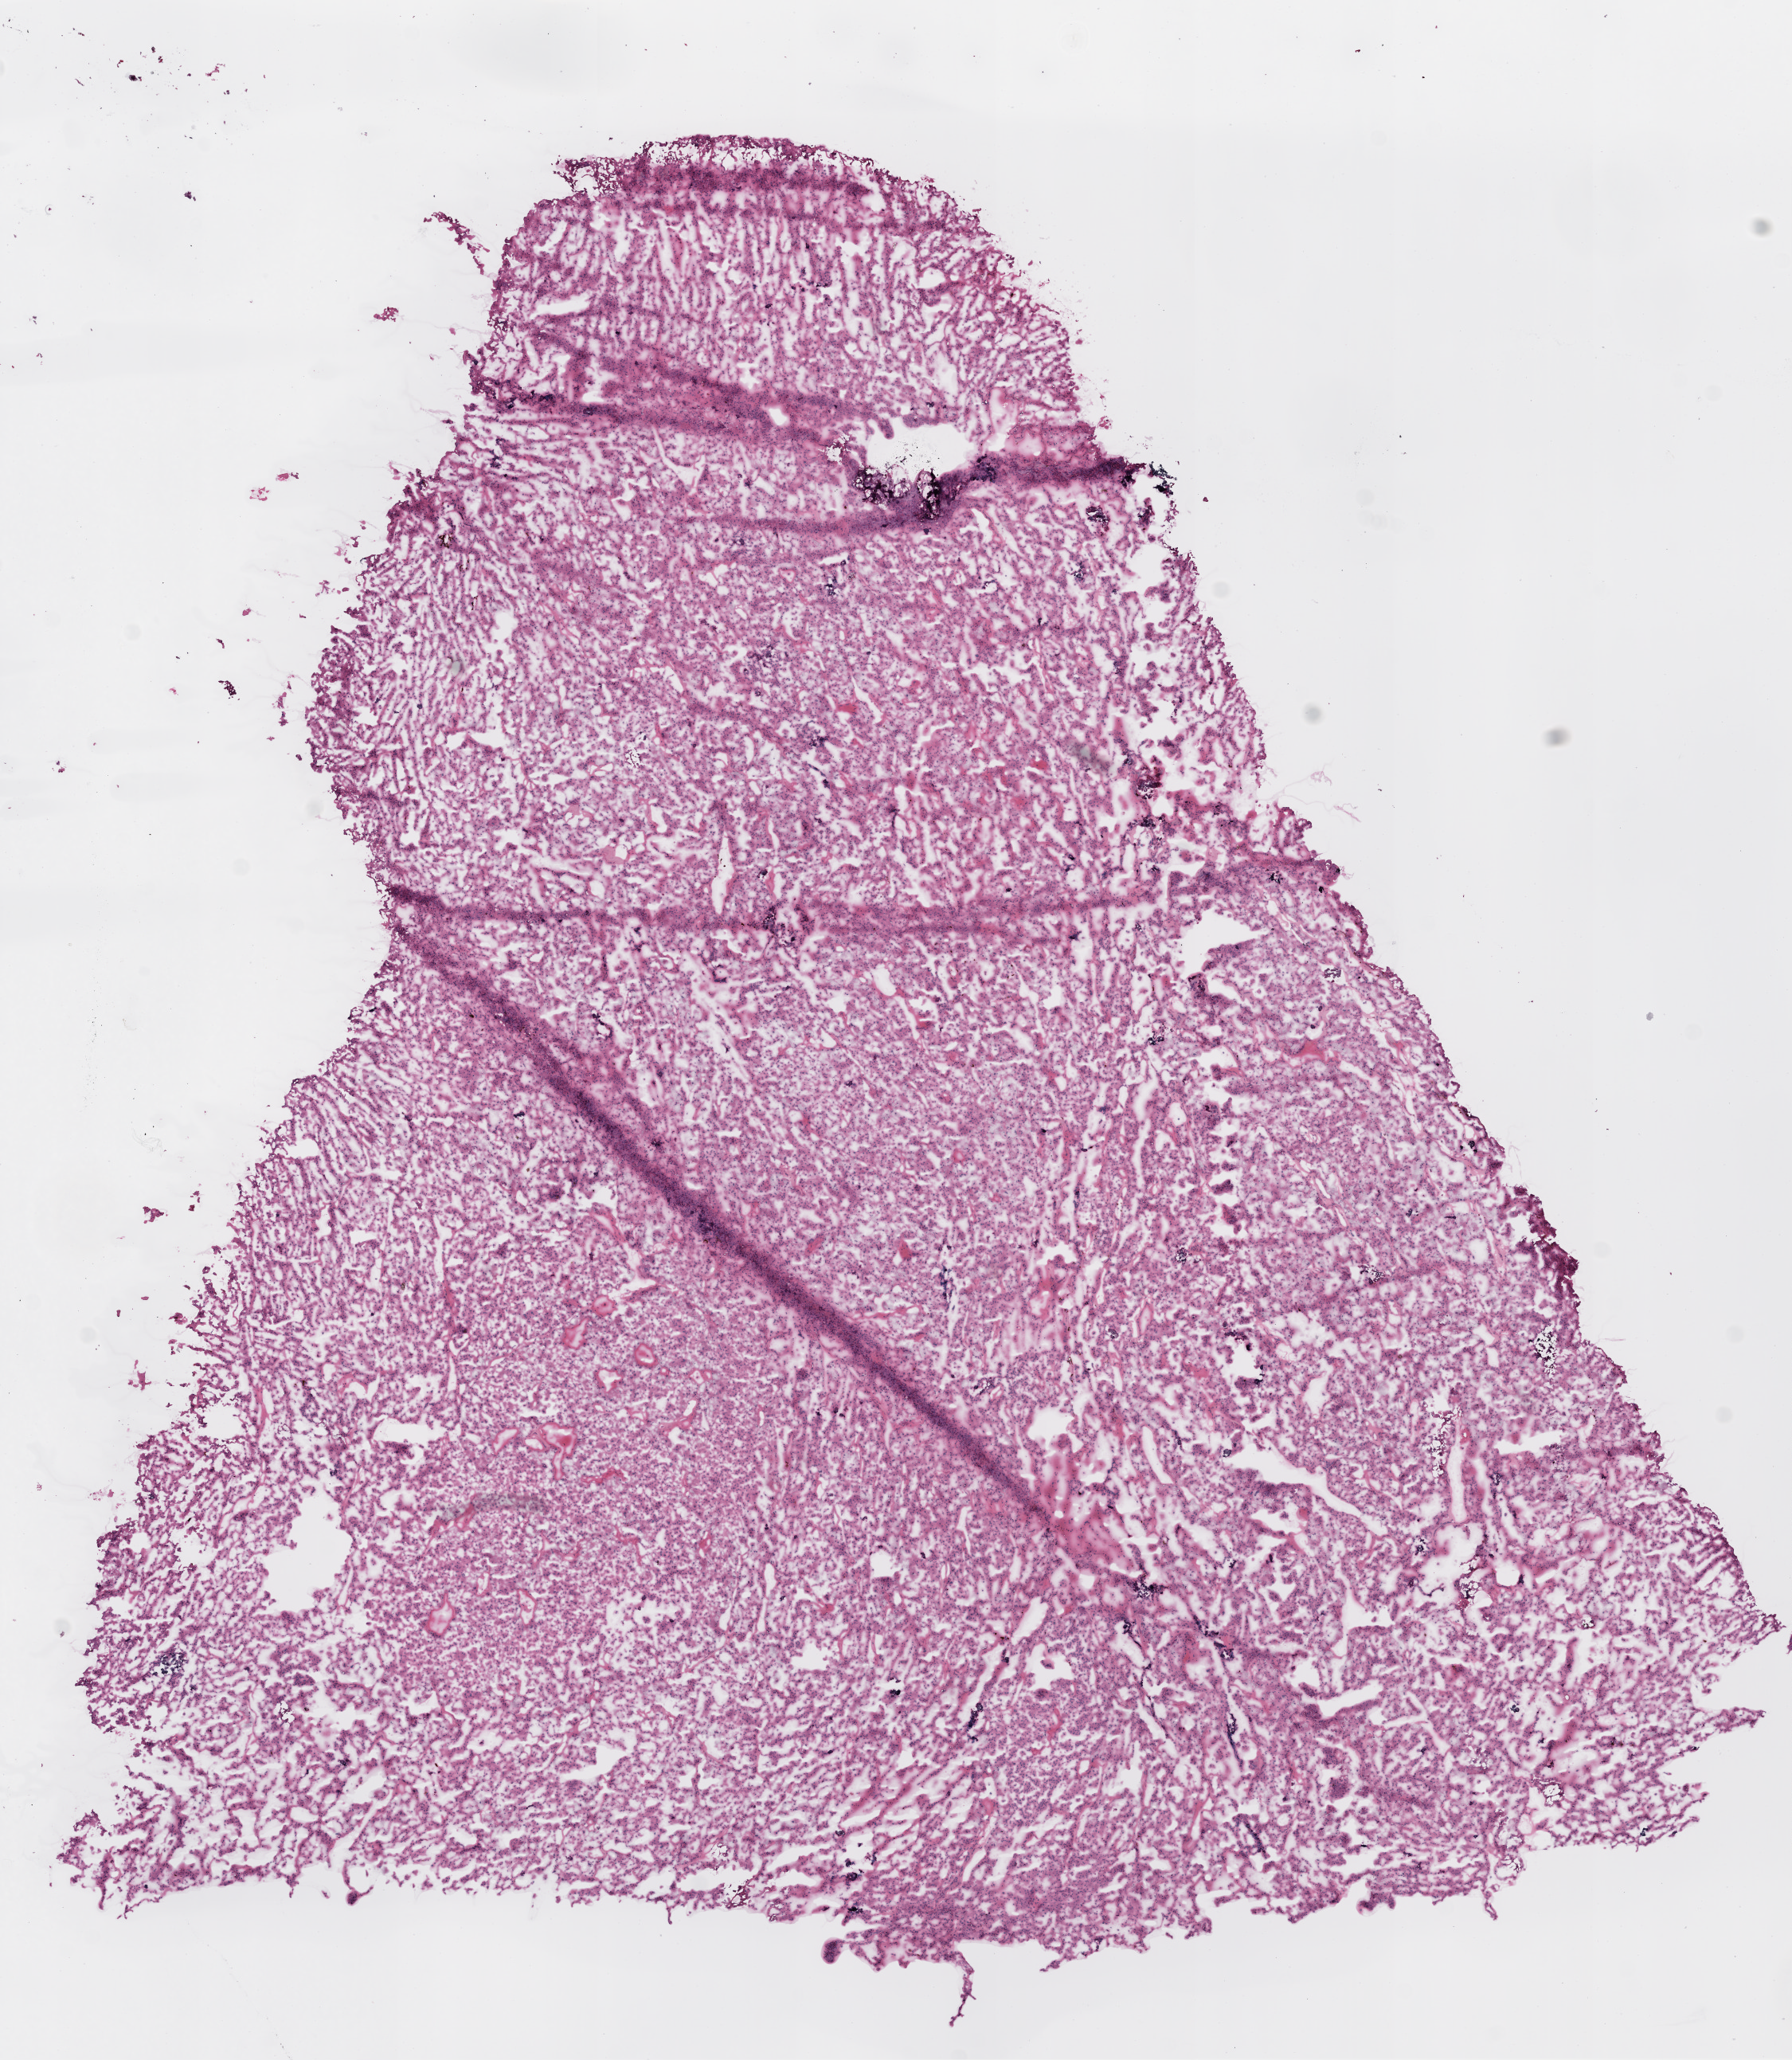
Digitized H&E-stained tissue section (whole slide), shown as a low-resolution overview of the whole scanned area (about 9.0 x 10.4 mm, from a 20x scan); frozen section; kidney, primary tumour sample. Patient: male, age at initial diagnosis 58 years. Histologic grade: G3 (poorly differentiated). Composition of this section per pathologist review: tumour nuclei 85%, normal cells 0%, stromal cells 5%, necrosis 0%.
- histologic diagnosis: Clear cell adenocarcinoma, NOS
- AJCC pathologic stage: I